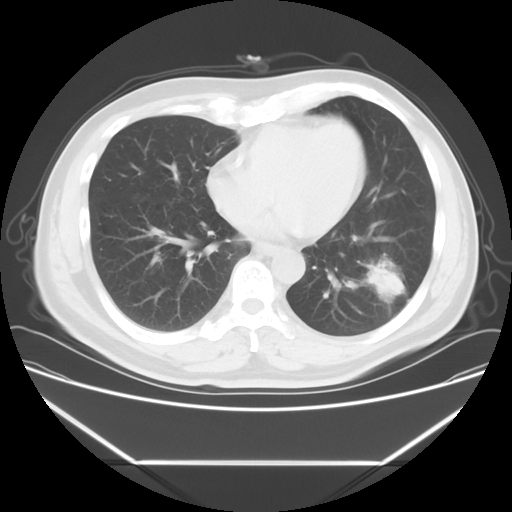
Chest CT, one axial slice; 120 kVp; lung window (W 1500 / L -600 HU); 512 × 512 image matrix, field of view 384 × 384 mm. Male patient, age 53 years. From the clinical record (not read from this slice): clinical TNM (as recorded): T1c N0 M0; histopathological grade: G2-3.
Outlined on this slice (bounding box drawn by a radiologist):
- lung tumour (recorded histology: adenocarcinoma): bounding box <363,245,409,314> (left, top, right, bottom; pixels)